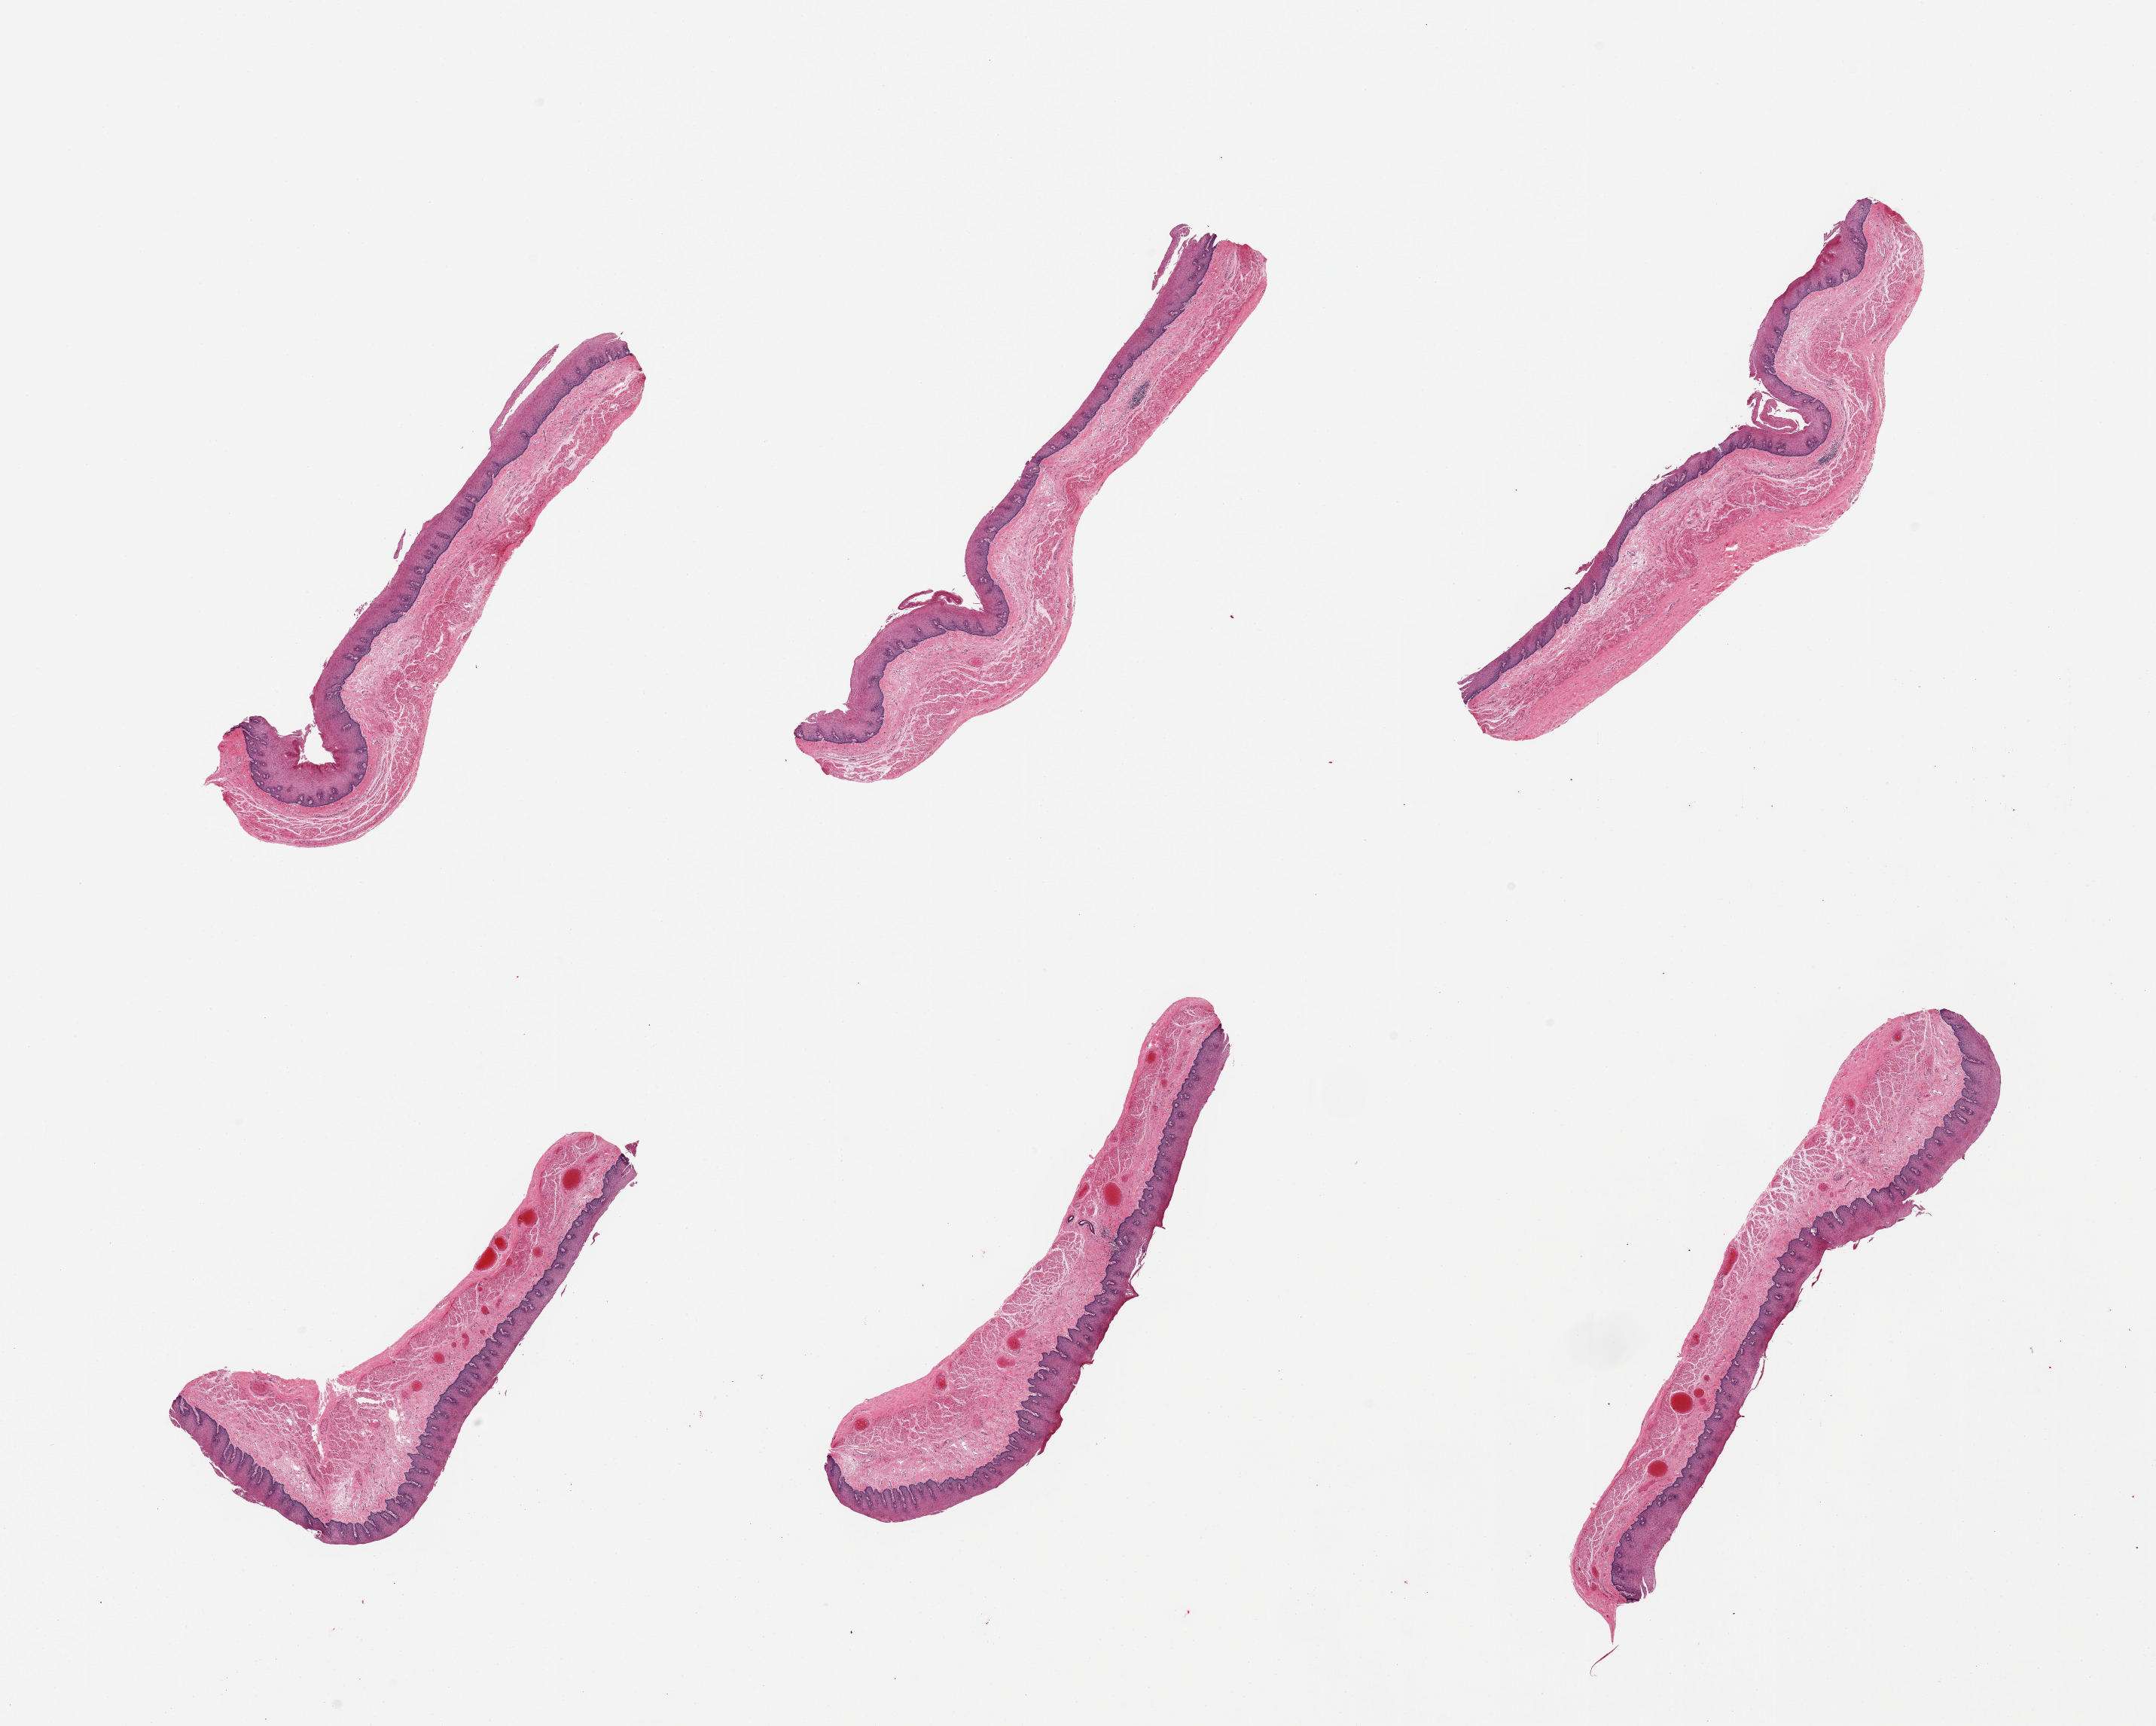
H&E whole-slide image — shown as a low-resolution overview of the whole scanned area (about 22.6 x 18.1 mm); PAXgene-fixed paraffin-embedded (PFPE) section; sampled site (target tissue): esophageal mucous membrane; donor tissue sample. Donor sex: female.
* review note (as recorded): 6 pieces; ~0.25mm squamous epithelium; congestion